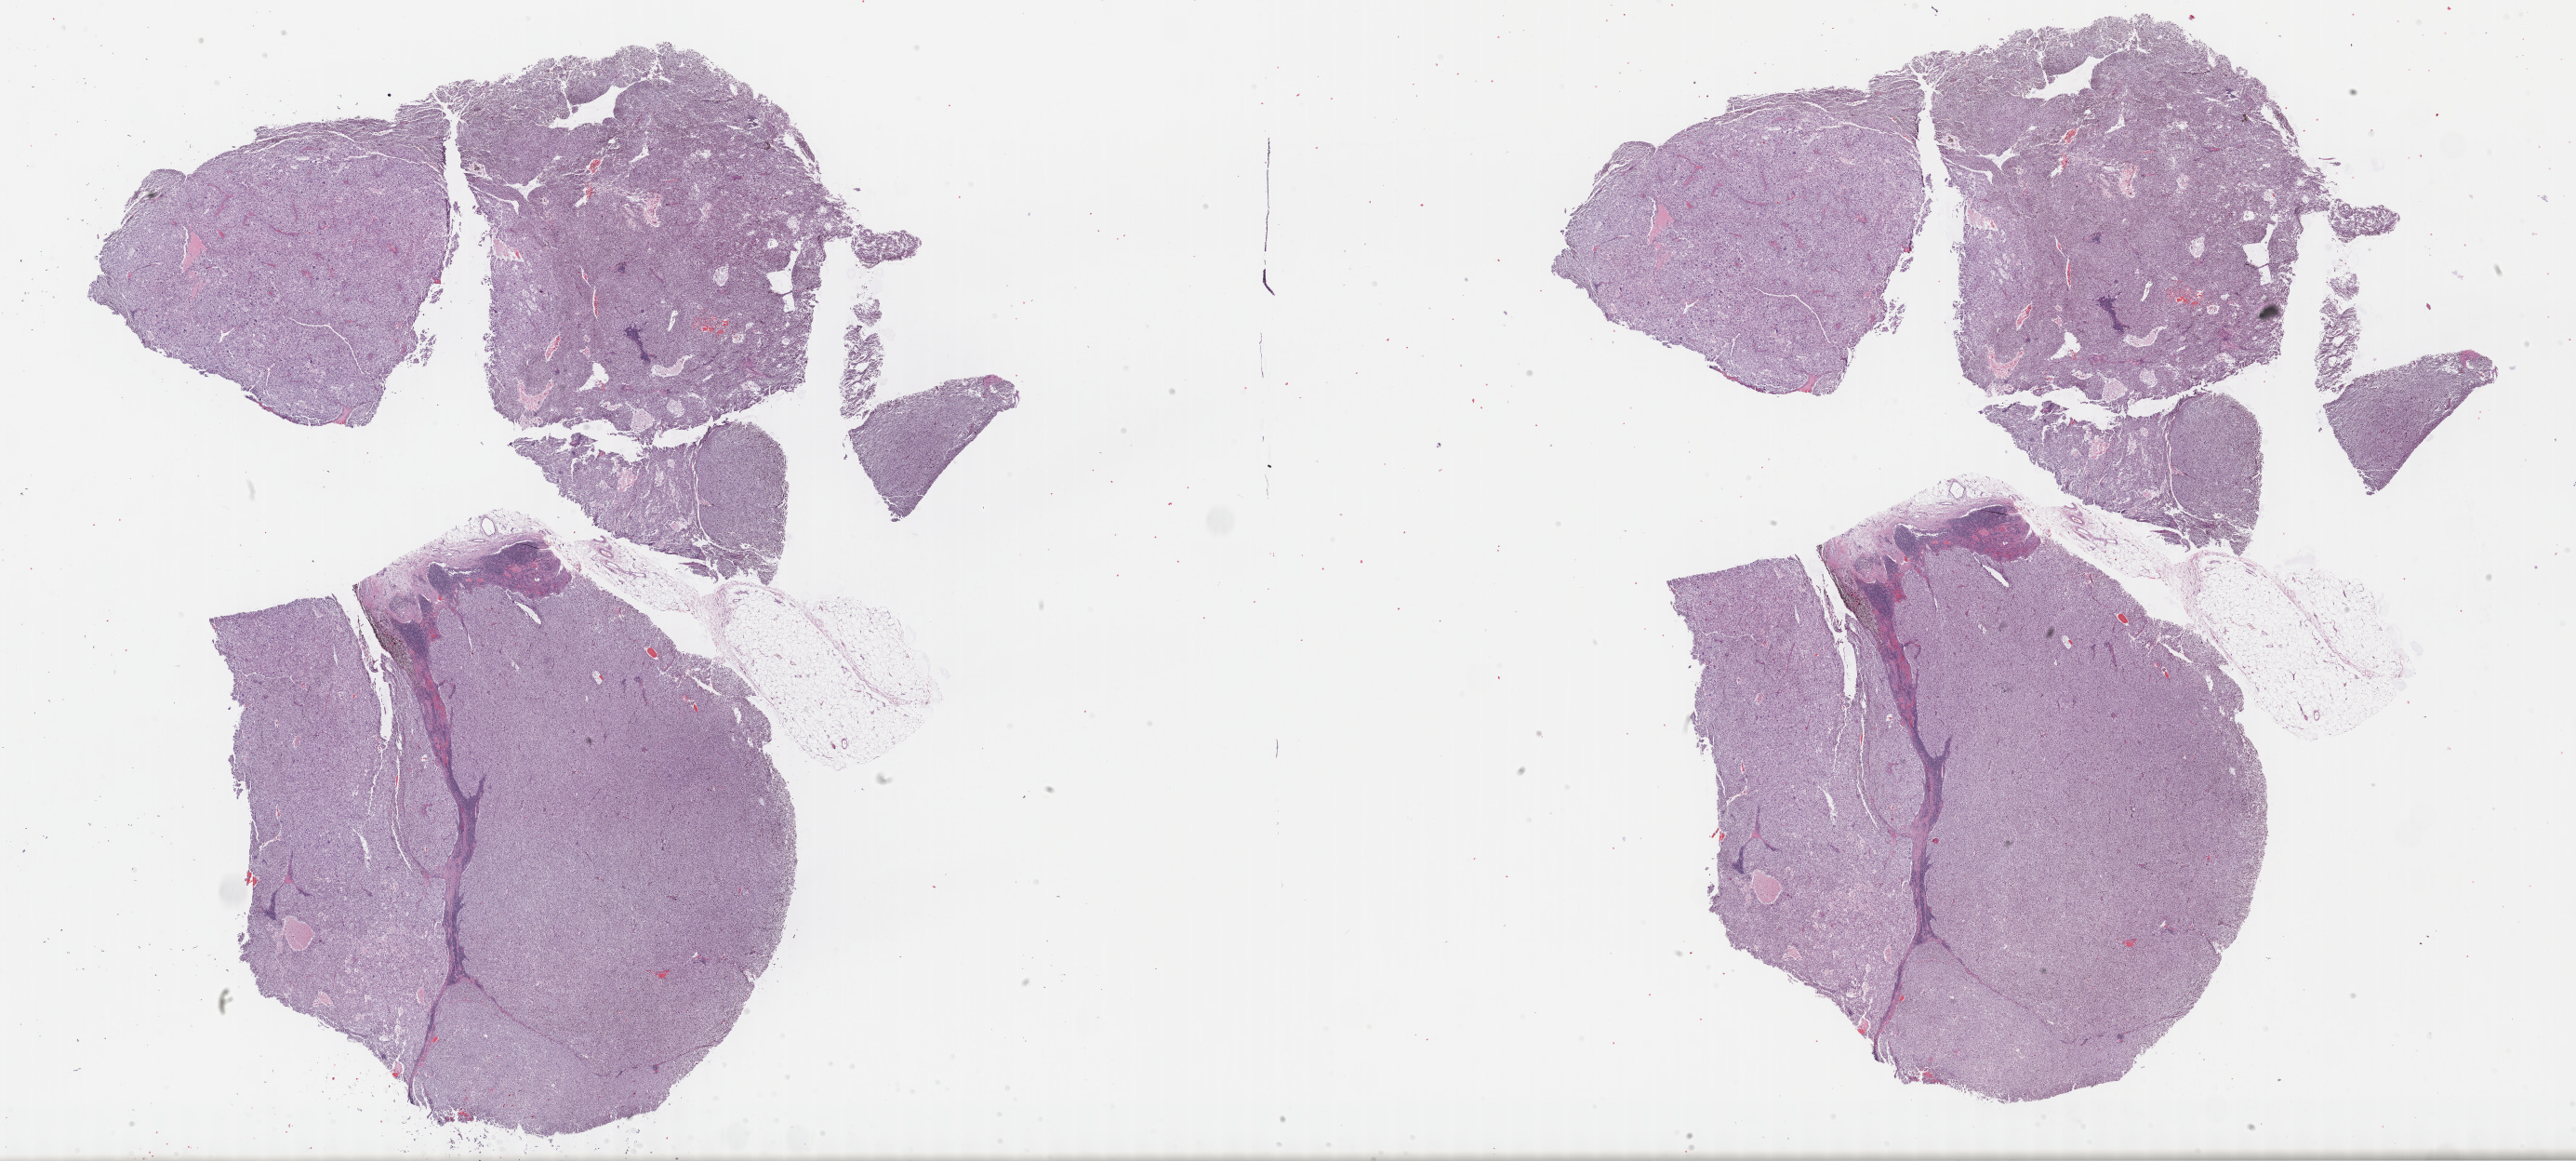
Digitized H&E tissue section (whole slide) — shown as a low-resolution overview of the whole scanned area (about 44.8 x 20.2 mm, acquisition: 40x scan), formalin-fixed paraffin-embedded (FFPE) diagnostic section, metastatic tumour sample, sampled site: pelvic lymph nodes. Female, age 68 years at initial diagnosis.
This section: metastatic tumour tissue. Patient diagnosis: Malignant melanoma, NOS.